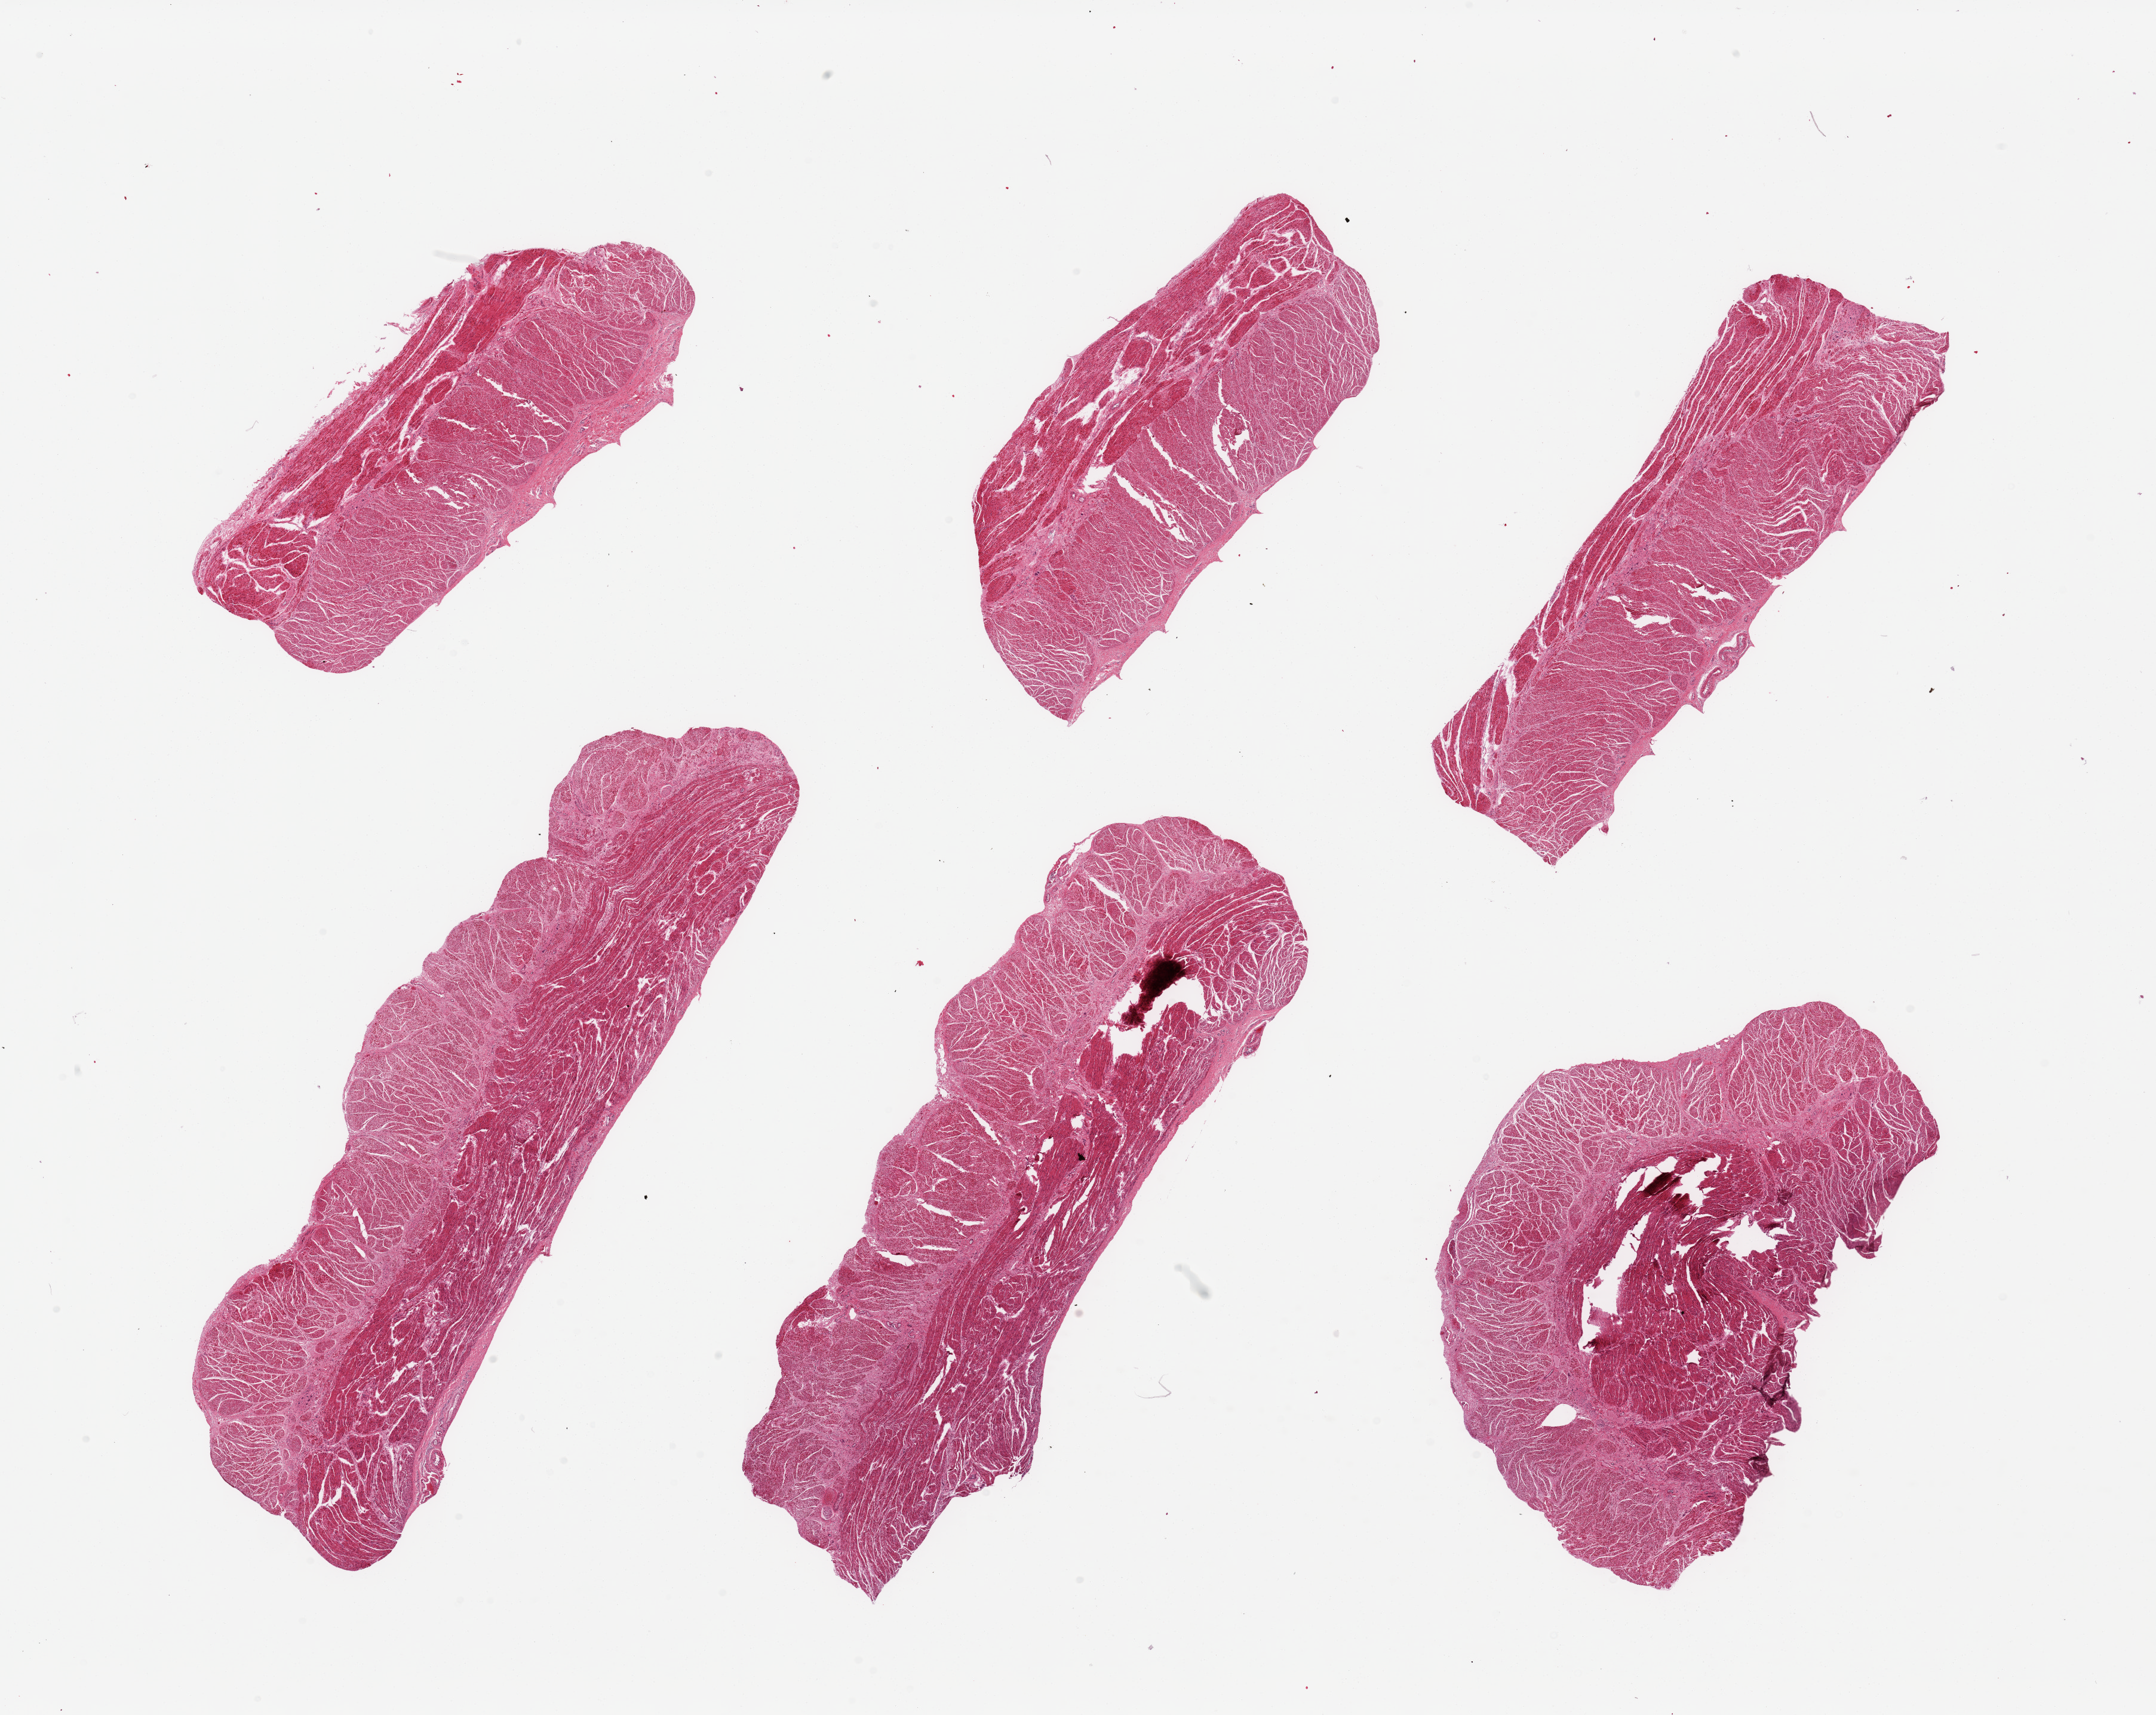
Digitized H&E-stained section, low-resolution overview of the scanned area, about 28.5 x 22.7 mm (slide scanned at 20x). PAXgene-fixed paraffin-embedded (PFPE) section. Section of gastroesophageal junction (target tissue). Donor tissue sample.
Review note (as recorded): 6 pieces; well dissected muscularis propria.